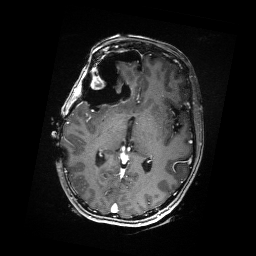
Brain MRI from a brain-tumour surgery series, one axial slice; position 93 of 176 along the scan axis; T1-weighted post-contrast; 1 mm slice thickness; 256 × 256 image matrix, field of view 256 × 256 mm. Case-level facts recorded for this patient, not image findings: histopathology: Metastatic Carcinoma from Breast primary; tumour location: Right Frontal.
Outlined on this slice (expert manual segmentation):
- residual tumour: bounding box <88,68,117,103> (left, top, right, bottom; pixels)